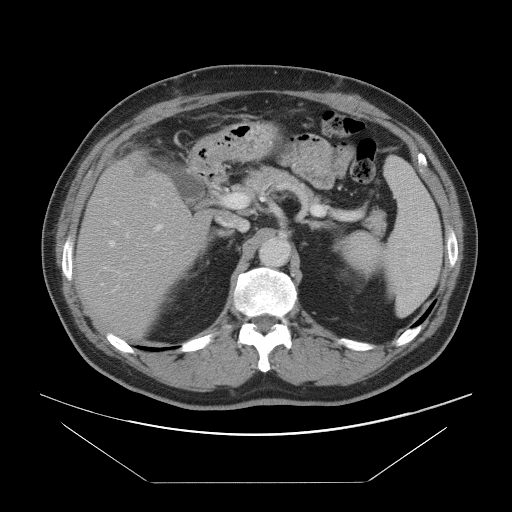
Contrast-enhanced abdominal CT, one axial slice. Position 53 of 97 along the scan axis. Intravenous contrast given. Soft-tissue window (W 400 / L 40 HU). 512 × 512 image matrix, field of view 442 × 442 mm. Male patient, age 62 years. Case-level facts recorded for this patient, not image findings: diagnosis: colorectal cancer liver metastases, imaged before liver resection; multiple liver metastases: no; largest metastasis: 7 cm; disease in both lobes: yes.
Annotated regions visible in this slice (outlined manually by an expert reader):
- hepatic veins: box from (x=109, y=233) to (x=174, y=258) px
- liver: (x=77, y=155)–(x=210, y=337)
- planned liver remnant (the part of the liver to remain after resection): (x=77, y=175)–(x=210, y=338)
- portal vein (with intrahepatic branches): (x=114, y=196)–(x=228, y=272)
- liver metastasis: (x=135, y=168)–(x=150, y=177)